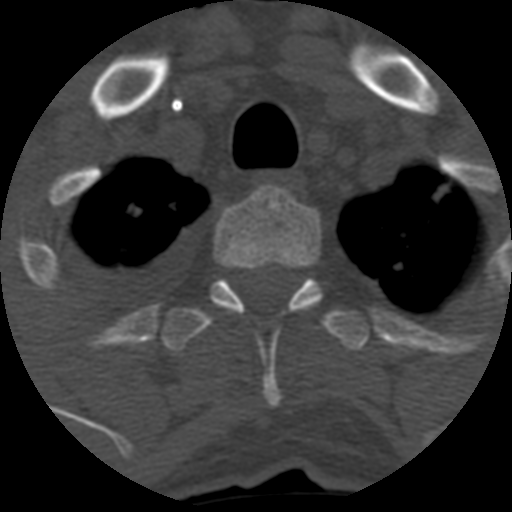
CT including the spine, one axial slice. Slice 497 of 708 in the series (ordered by position). 120 kVp. One of 3 acquisitions stored at this slice position. Bone window (W 1800 / L 400 HU). 1.25 mm slice thickness. 512 × 512 image matrix. Patient age 55 years. From the clinical record (not read from this slice): primary cancer: colon; vertebrae with lytic lesions (as recorded): T12, L1, L5.
Outlined on this slice (semi-automatically segmented with operator editing):
- T2 vertebra: bounding box [x1, y1, x2, y2] px = [213, 186, 321, 406]
- T3 vertebra: [161, 278, 369, 352]